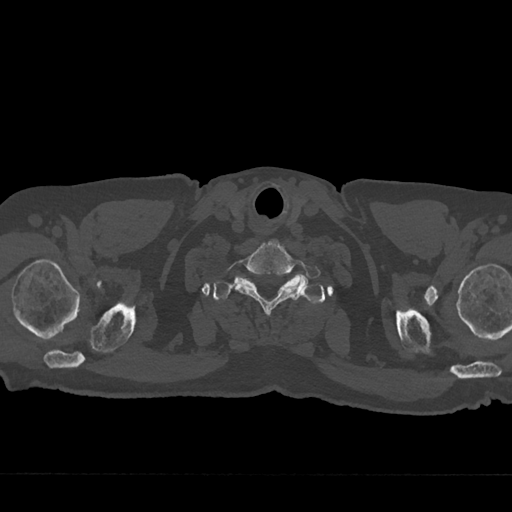
CT including the spine, one axial slice; slice 681 of 797 in the series (ordered by position); 120 kVp; bone window (W 1800 / L 400 HU); 512 × 512 image matrix, field of view 377 × 377 mm. Male patient, age 75 years. Case-level facts recorded for this patient, not image findings: primary cancer: renal.
Outlined on this slice (semi-automatic segmentation, software-assisted and operator-edited):
- T1 vertebra: box from (x=213, y=276) to (x=322, y=303) px